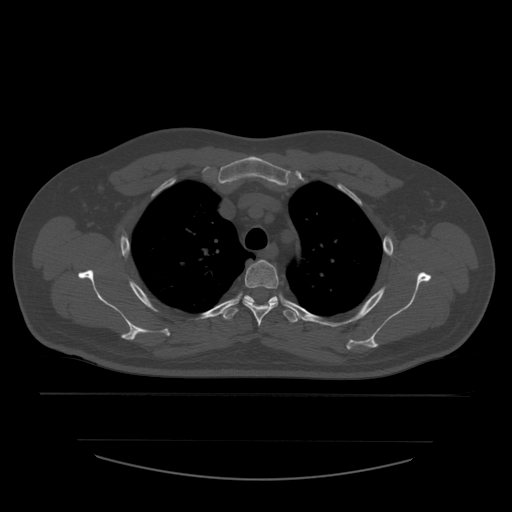
CT including the spine, one axial slice. Position 429 of 532 along the scan axis. Reconstruction kernel STANDARD. Bone window (W 1800 / L 400 HU). 512 × 512 image matrix. Patient age 44 years. Case-level facts recorded for this patient, not image findings: primary cancer: soft tissue sarcoma.
Annotated regions visible in this slice (semi-automatically segmented with operator editing):
- T3 vertebra: bounding box [x1, y1, x2, y2] px = [243, 260, 279, 327]
- T4 vertebra: [223, 295, 298, 323]